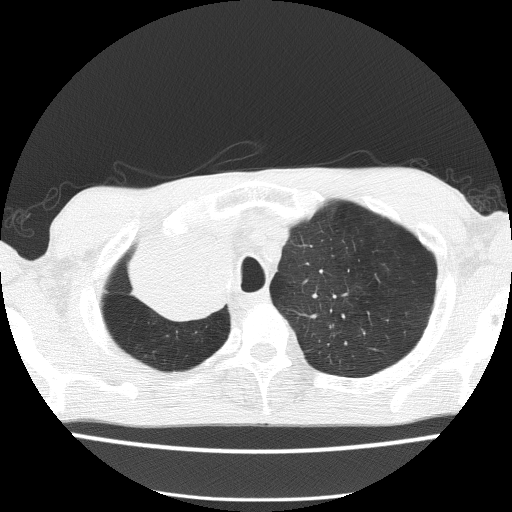
Chest CT (low-dose screening protocol), one axial image. Baseline annual screen. Lung window (W 1500 / L -600 HU). Lung (sharp) reconstruction kernel (FC51). Slice 28 of 150 in the series. Male participant, aged 59 years at enrolment. Former smoker at enrolment.
- Expert-annotated lung lesion, bounding box <127,235,242,329> (left, top, right, bottom; pixels).
- The screening reader recorded 5 non-calcified nodules or masses ≥4 mm on this exam (left upper lobe, left upper lobe, left upper lobe, right middle lobe, right lower lobe); which of them this box marks is not recorded.
- Later outcome: lung cancer diagnosed 72 days after this screen — squamous cell carcinoma, NOS, right upper lobe, moderately differentiated (G2), stage IV (AJCC 6th edition).